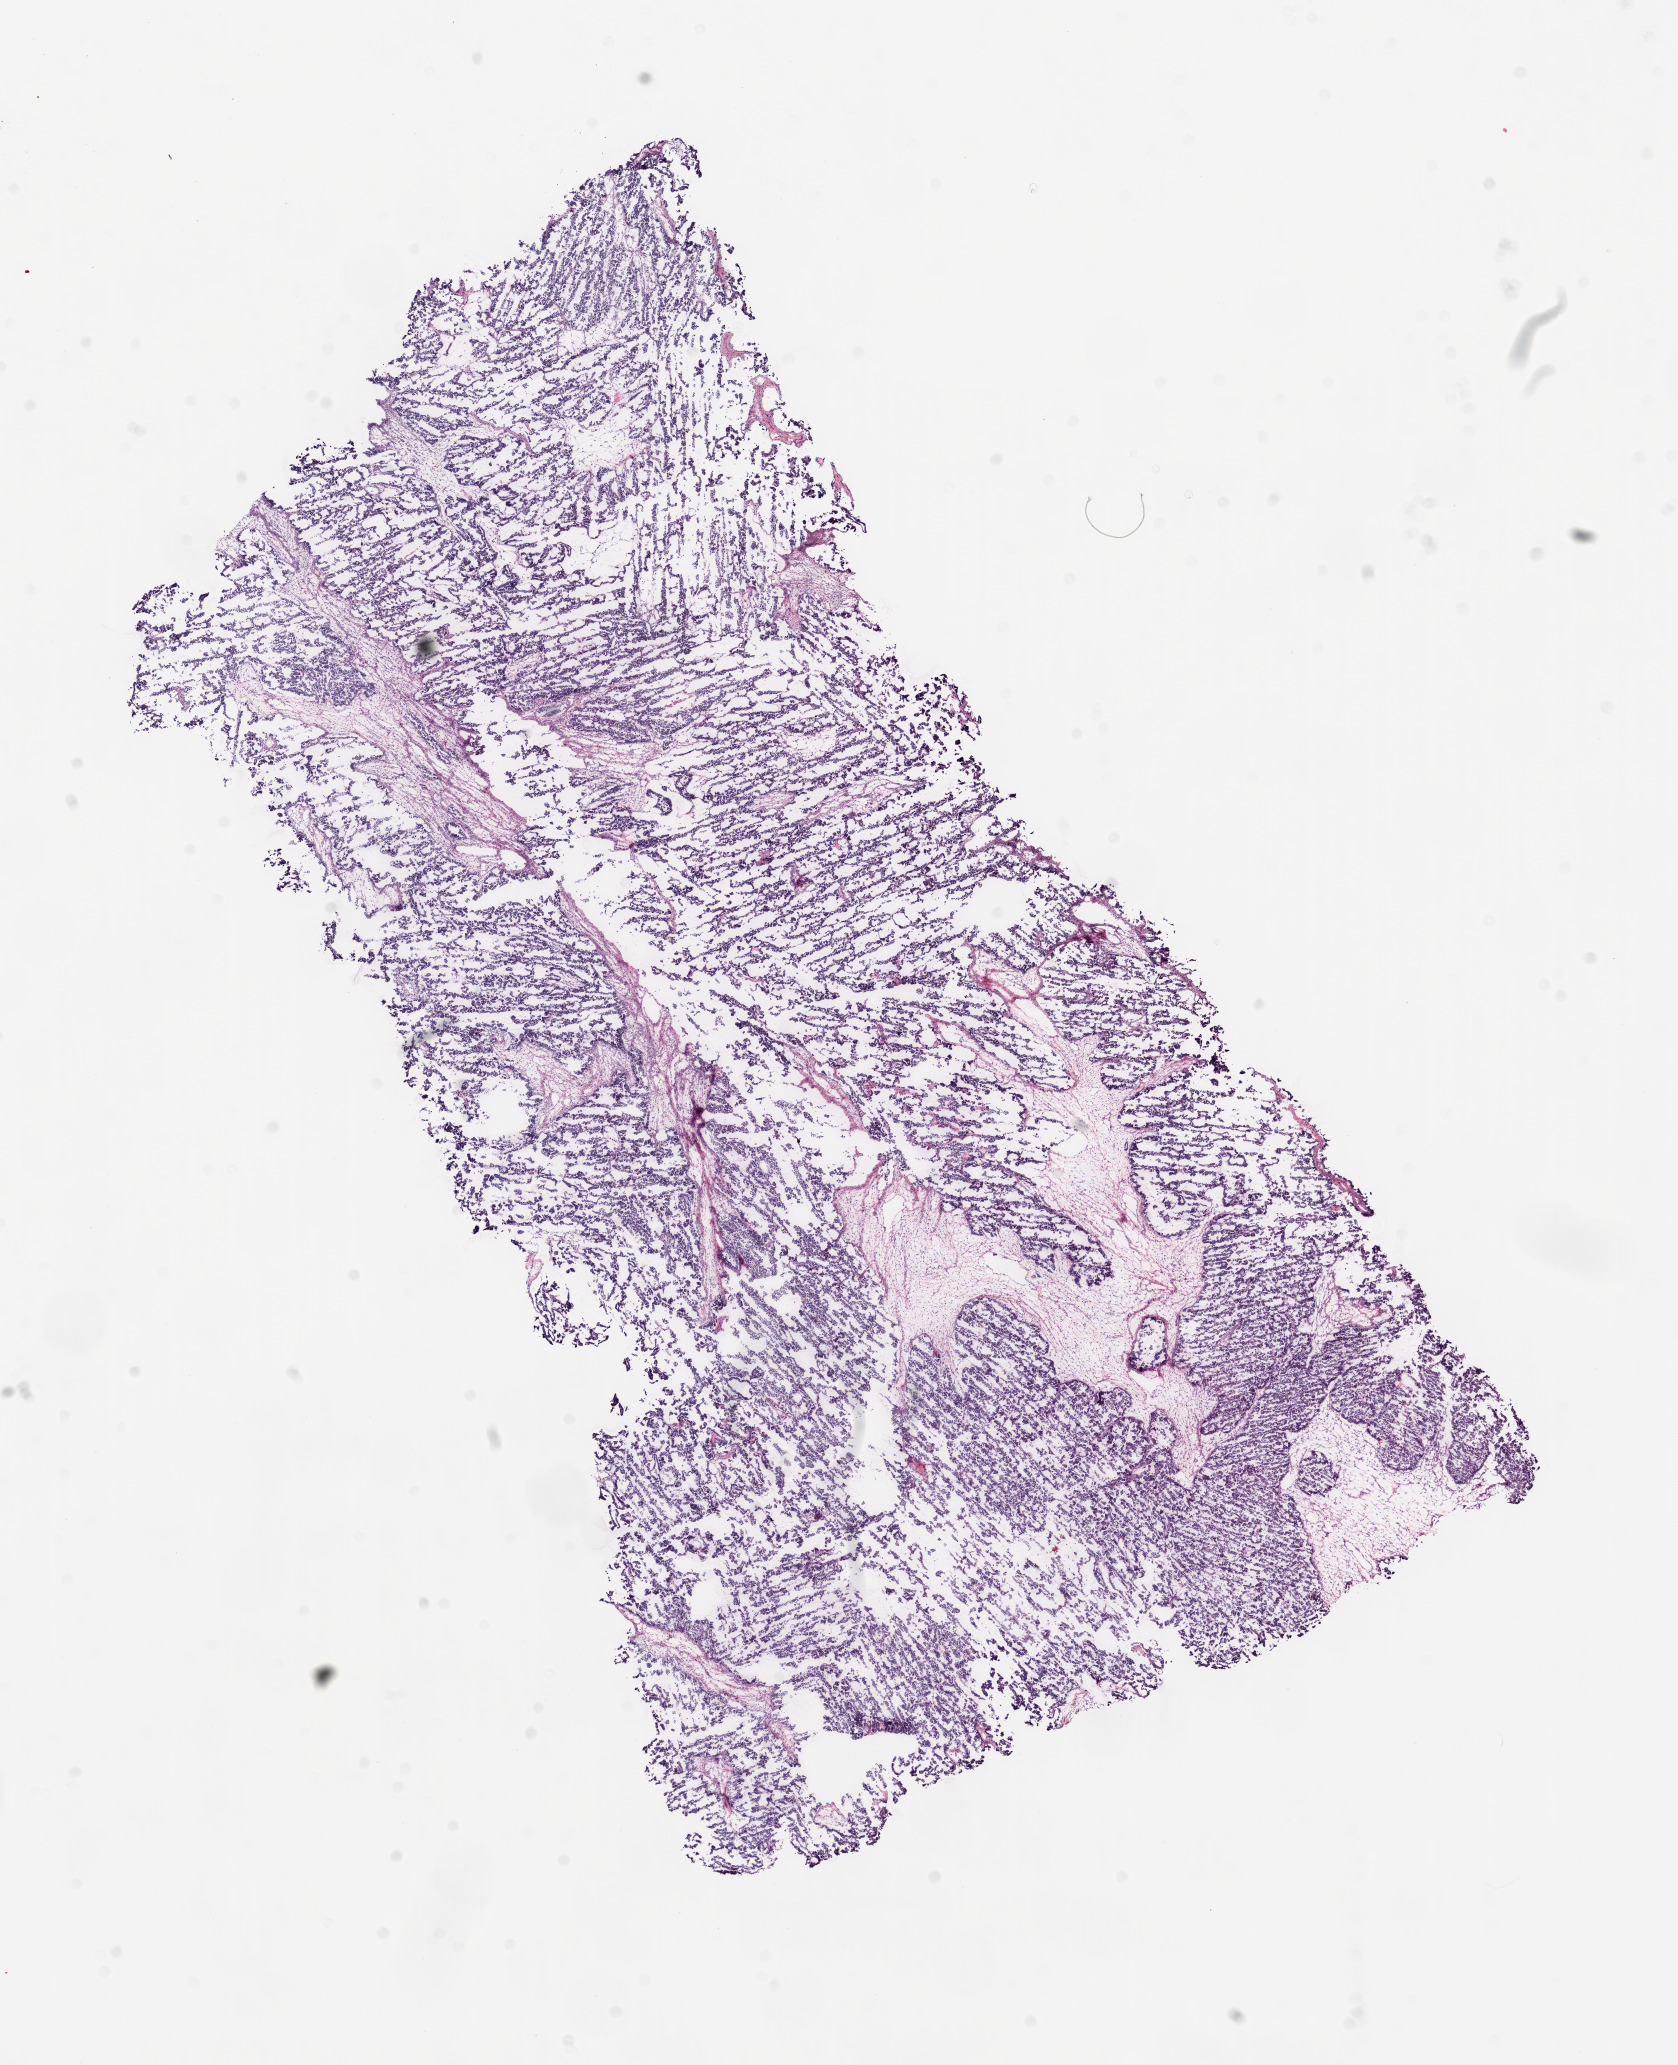
Digitized H&E-stained tissue section (whole slide) — whole scanned area (about 13.5 x 16.7 mm) shown as a low-resolution overview, frozen section from the top of the tissue portion, ovary, primary tumour sample. Patient: female, age at initial diagnosis 58 years. Histologic grade: G3 (poorly differentiated). Pathologist review of this section (percent, as recorded): tumour cells 90%, tumour nuclei 95%, normal cells 0%, stromal cells 8%, necrosis 2%. Inflammatory infiltration, as recorded: lymphocyte infiltration 100%.
Diagnosis: Serous cystadenocarcinoma, NOS. Laterality: bilateral. FIGO stage: IIIC.